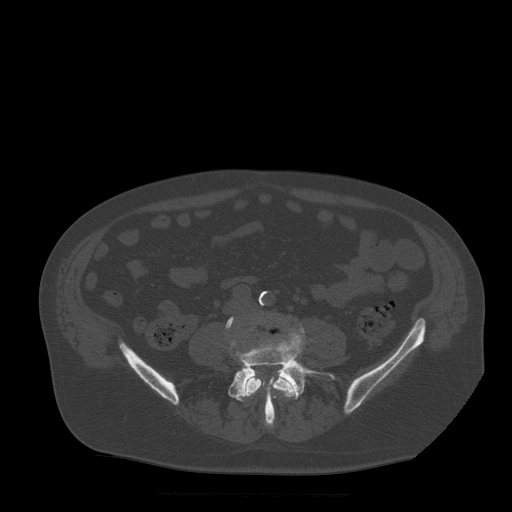
CT including the spine, one axial slice; slice 99 of 522 in the series (ordered by position); bone window (W 1800 / L 400 HU); 512 × 512 image matrix, field of view 420 × 420 mm. Patient age 72 years. From the clinical record (not read from this slice): primary cancer: prostate.
Structures marked on this image (semi-automatic segmentation, software-assisted and operator-edited):
- L4 vertebra: bounding box <244,370,297,398> (left, top, right, bottom; pixels)
- L5 vertebra: <226,316,336,425>